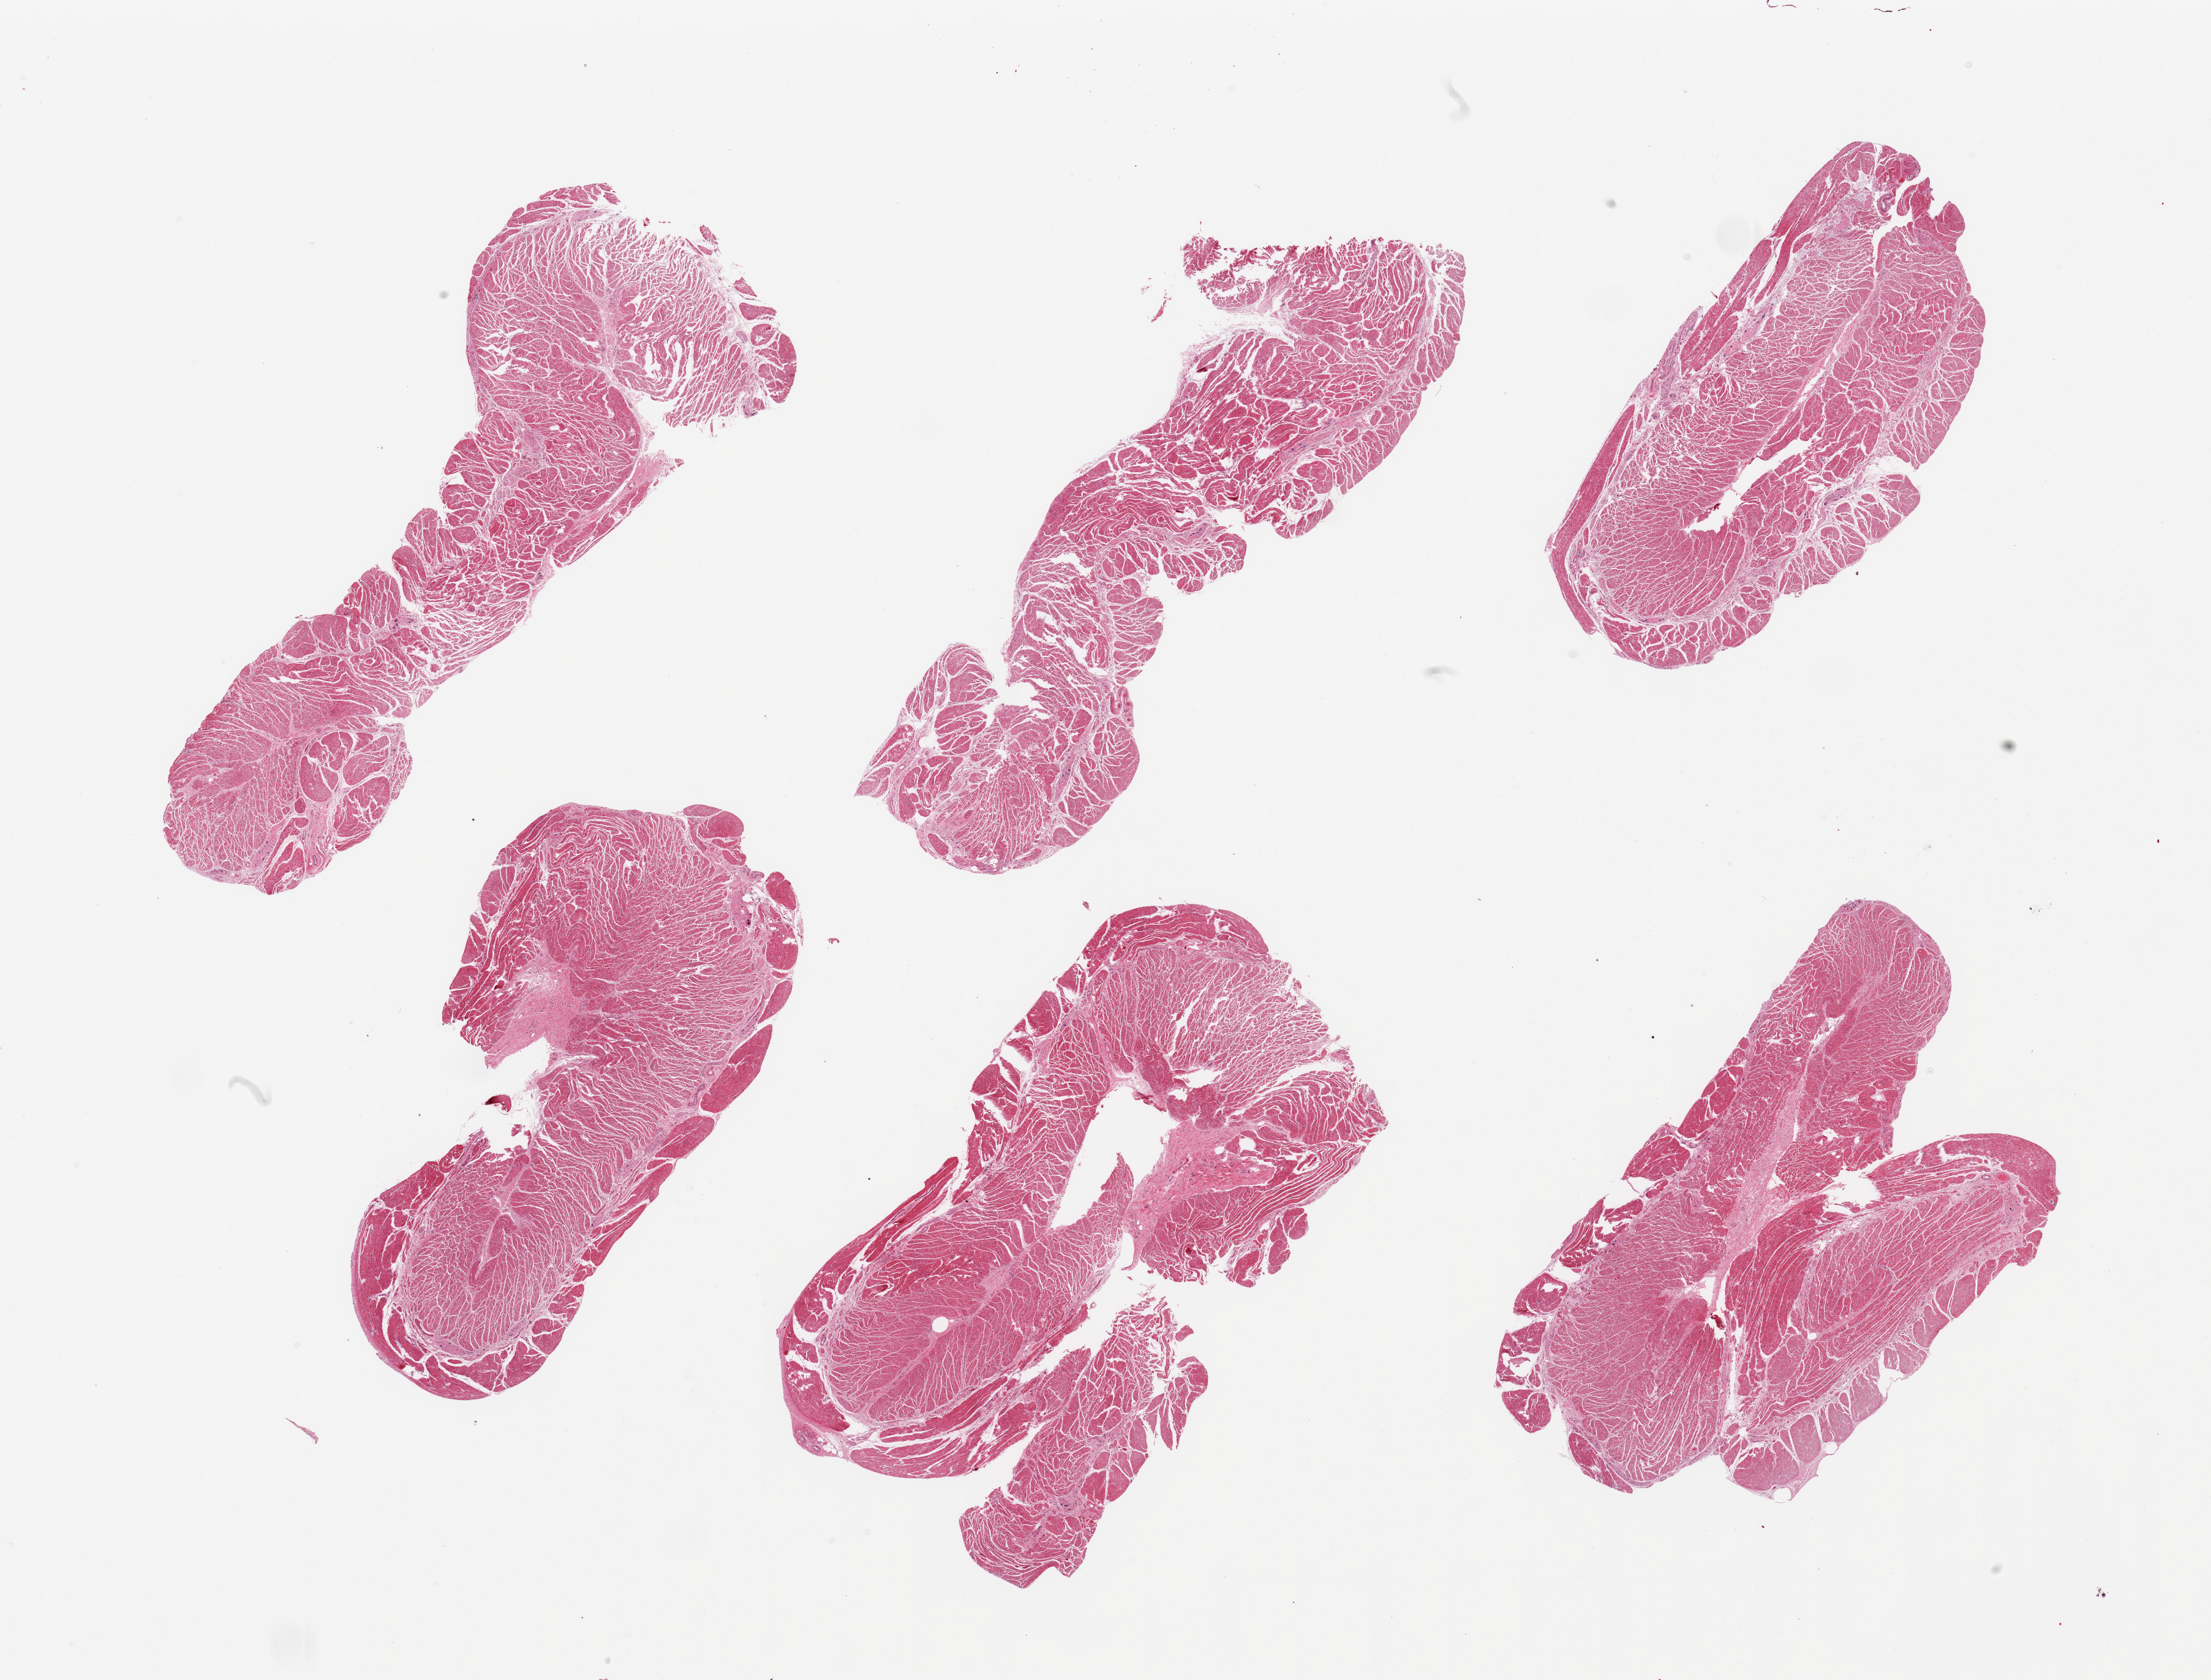
Digitized hematoxylin and eosin (H&E)-stained section, shown as a low-resolution overview of the whole scanned area (about 28.5 x 21.7 mm, slide scanned at 20x). PAXgene-fixed, paraffin-embedded tissue. Section of esophageal muscle (target tissue). Donor tissue sample. Female donor.
Pathologist's review note for this sample: 6 pieces, confirmed target muscularis.